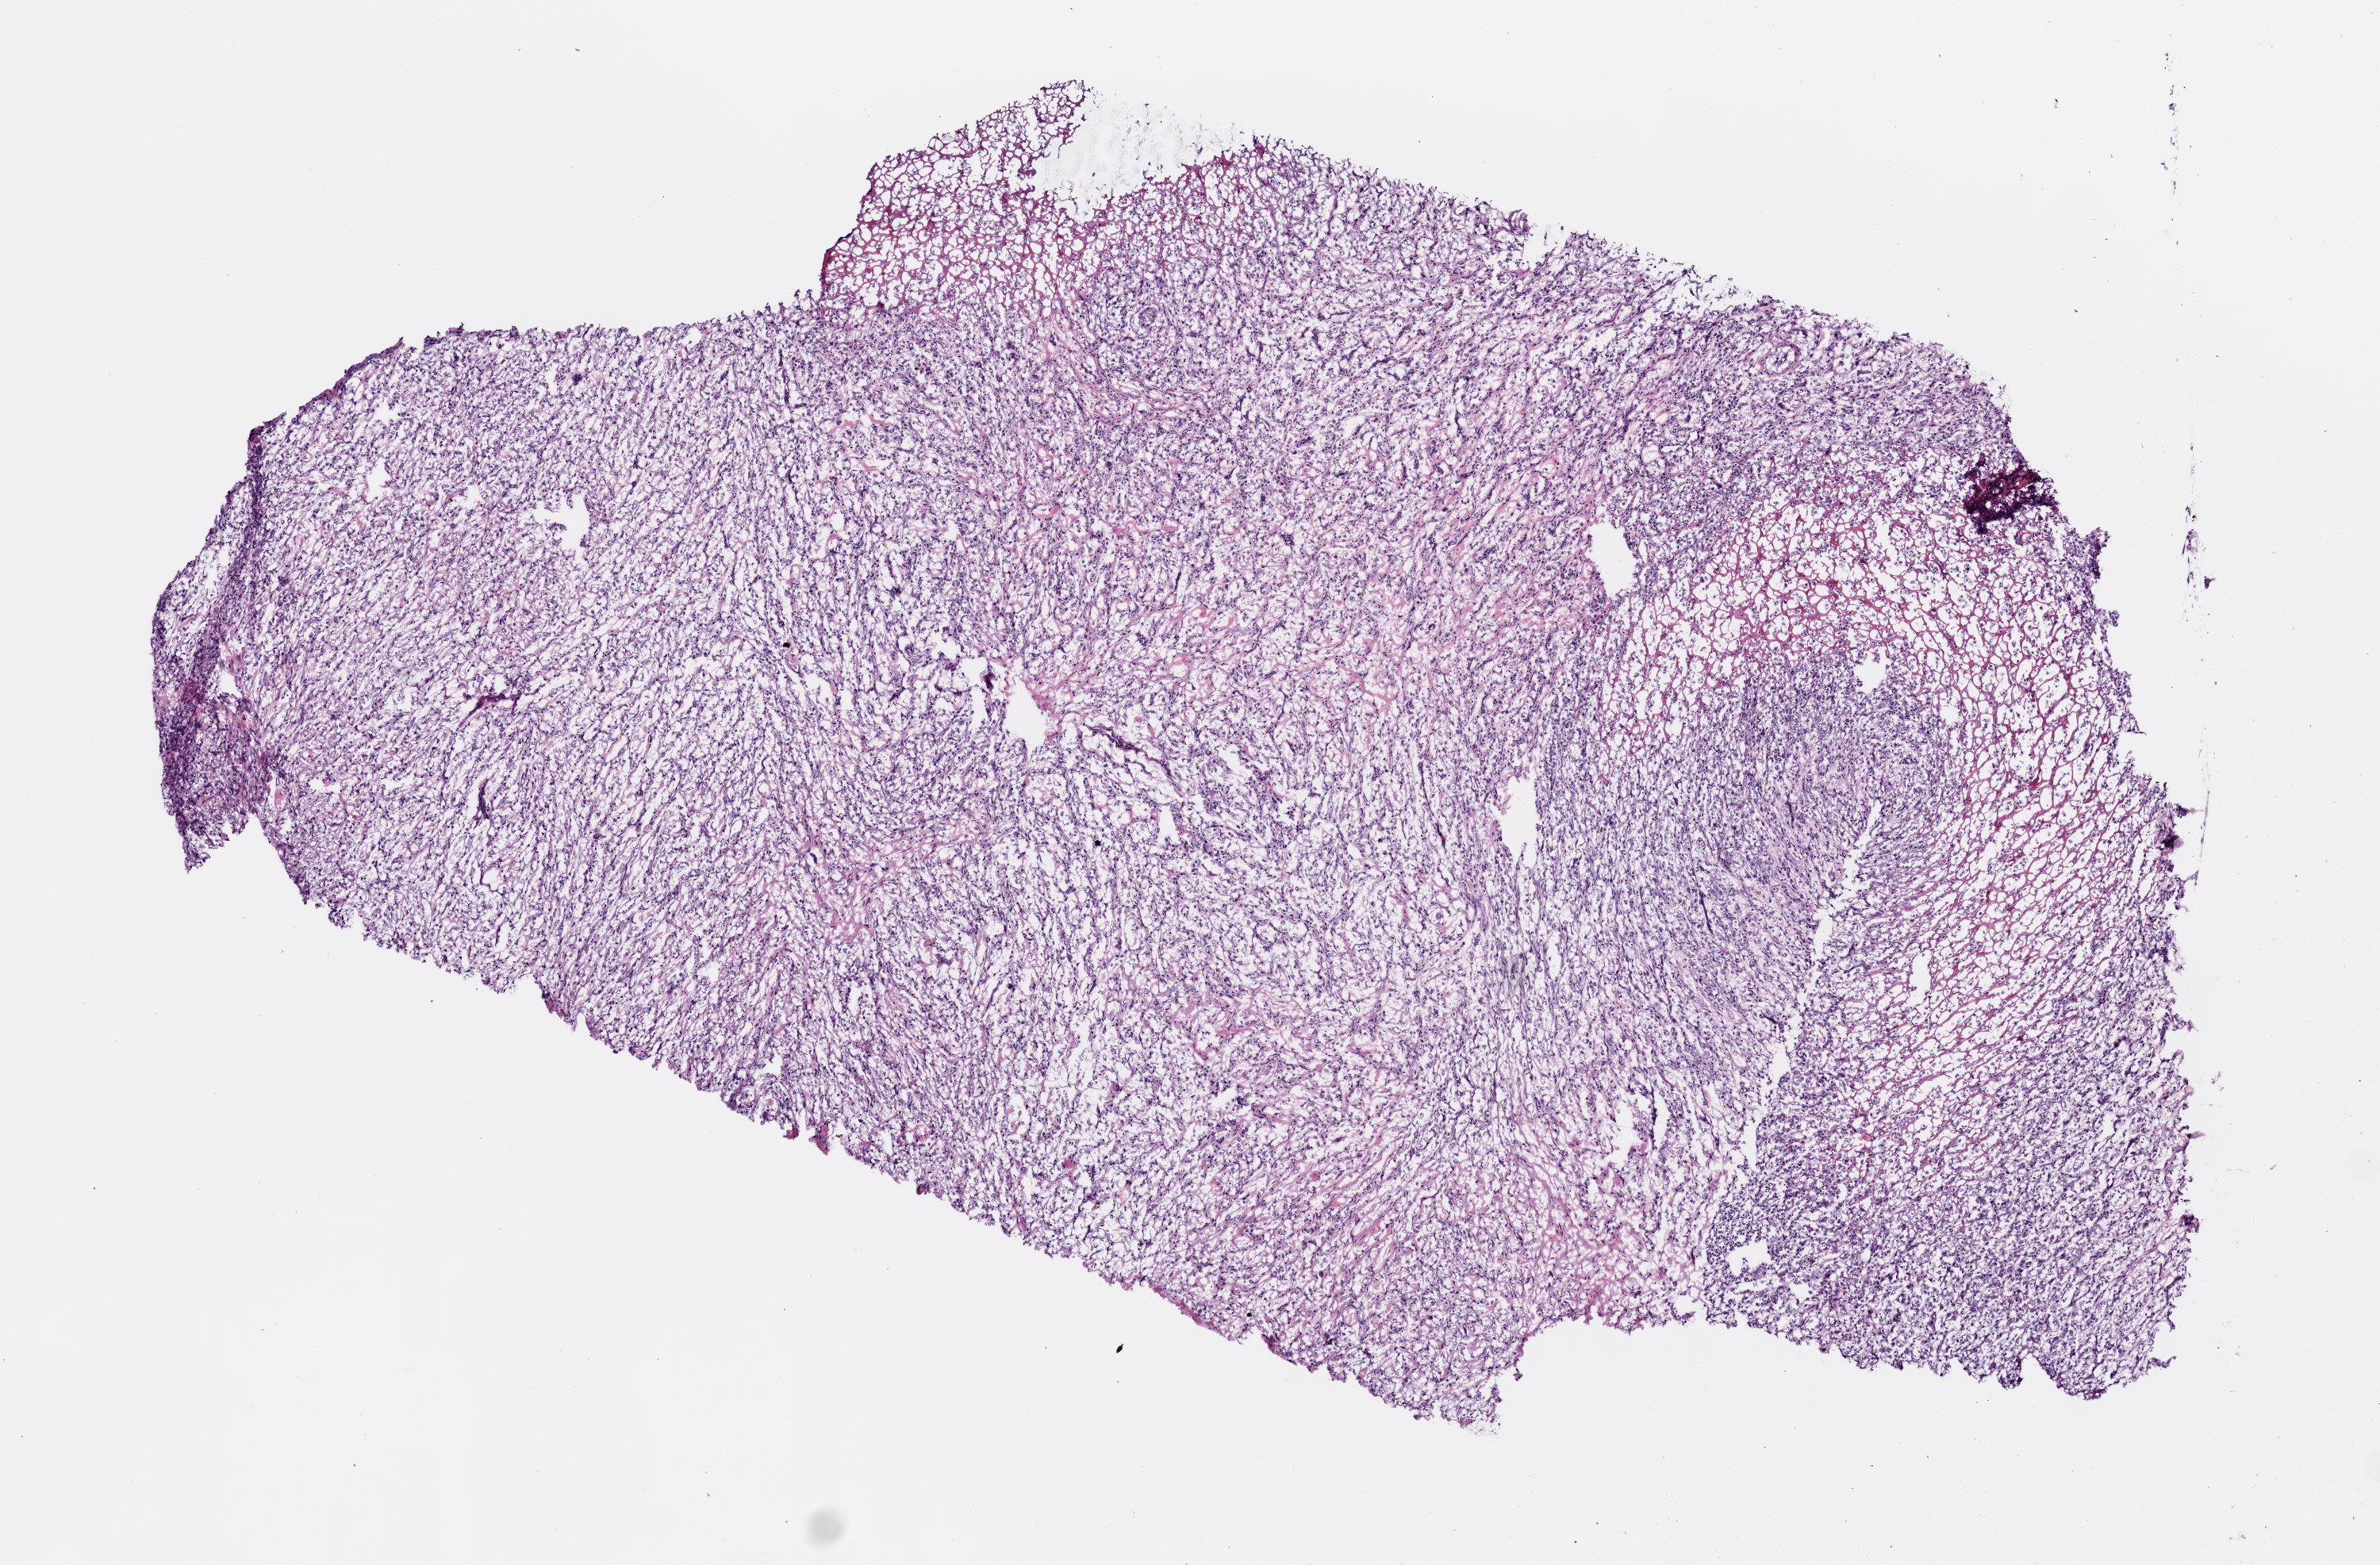
Digitized H&E-stained tissue section (whole slide) — low-resolution overview of the scanned area, about 6.0 x 4.0 mm, frozen section, stomach, primary tumour sample. Patient: female, age at initial diagnosis 72 years. Composition of this section per pathologist review: tumour cells 85%, tumour nuclei 70%.
Histologic diagnosis: Carcinoma, diffuse type.